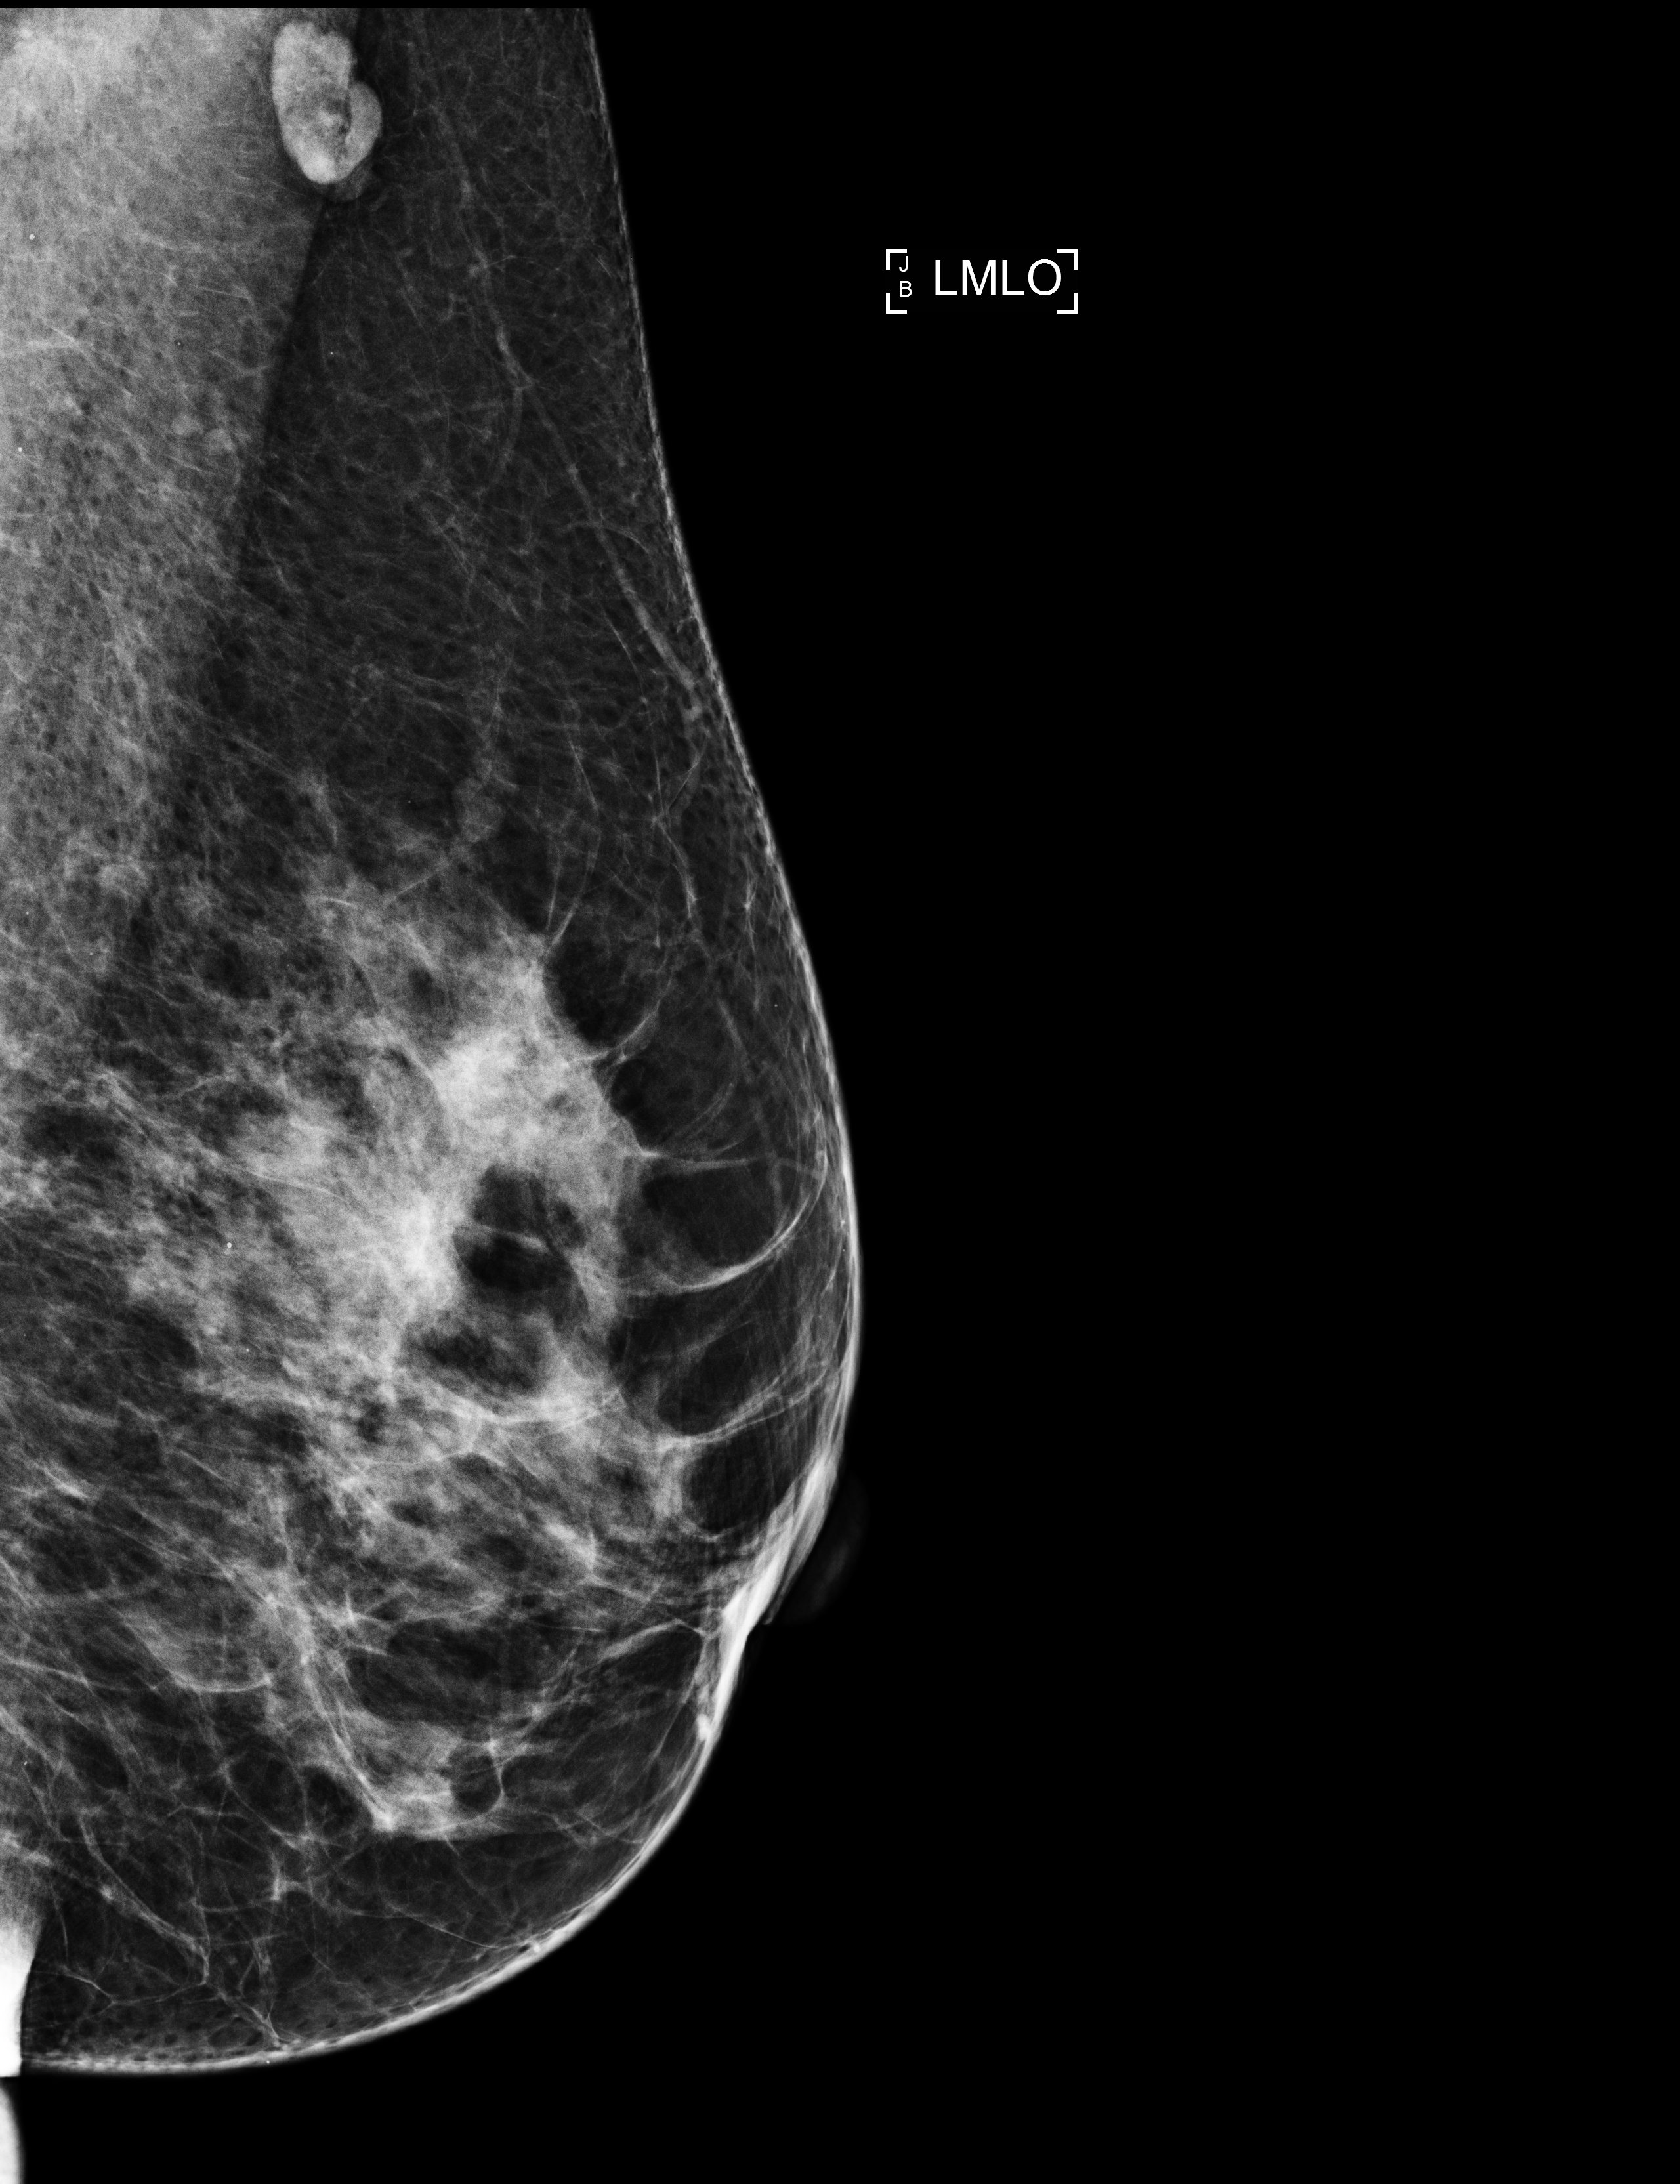
Screening examination; compressed breast thickness 59 mm. Patient aged 61 years (female).
Image type: full-field digital mammogram. Breast: left. Projection: medio-lateral oblique projection.